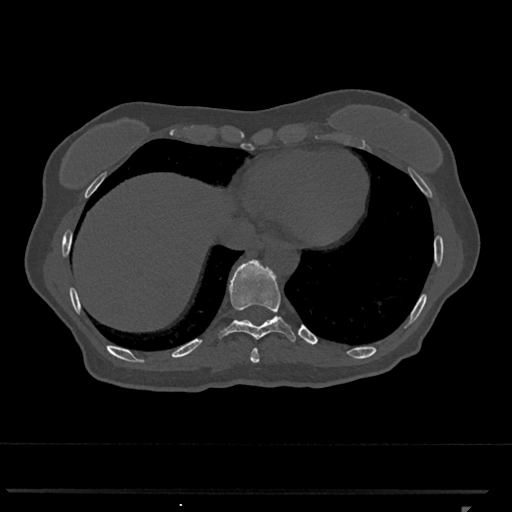
CT including the spine, one axial slice; position 570 of 793 along the scan axis; reconstruction kernel Br40s/3; 120 kVp; bone window (W 1800 / L 400 HU); 512 × 512 image matrix, field of view 380 × 380 mm. Female patient, age 62 years. Case-level facts recorded for this patient, not image findings: primary cancer: renal.
Structures marked on this image (semi-automatic segmentation, software-assisted and operator-edited):
- T10 vertebra: box from (x=219, y=260) to (x=296, y=342) px
- T9 vertebra: (x=250, y=349)–(x=260, y=363)